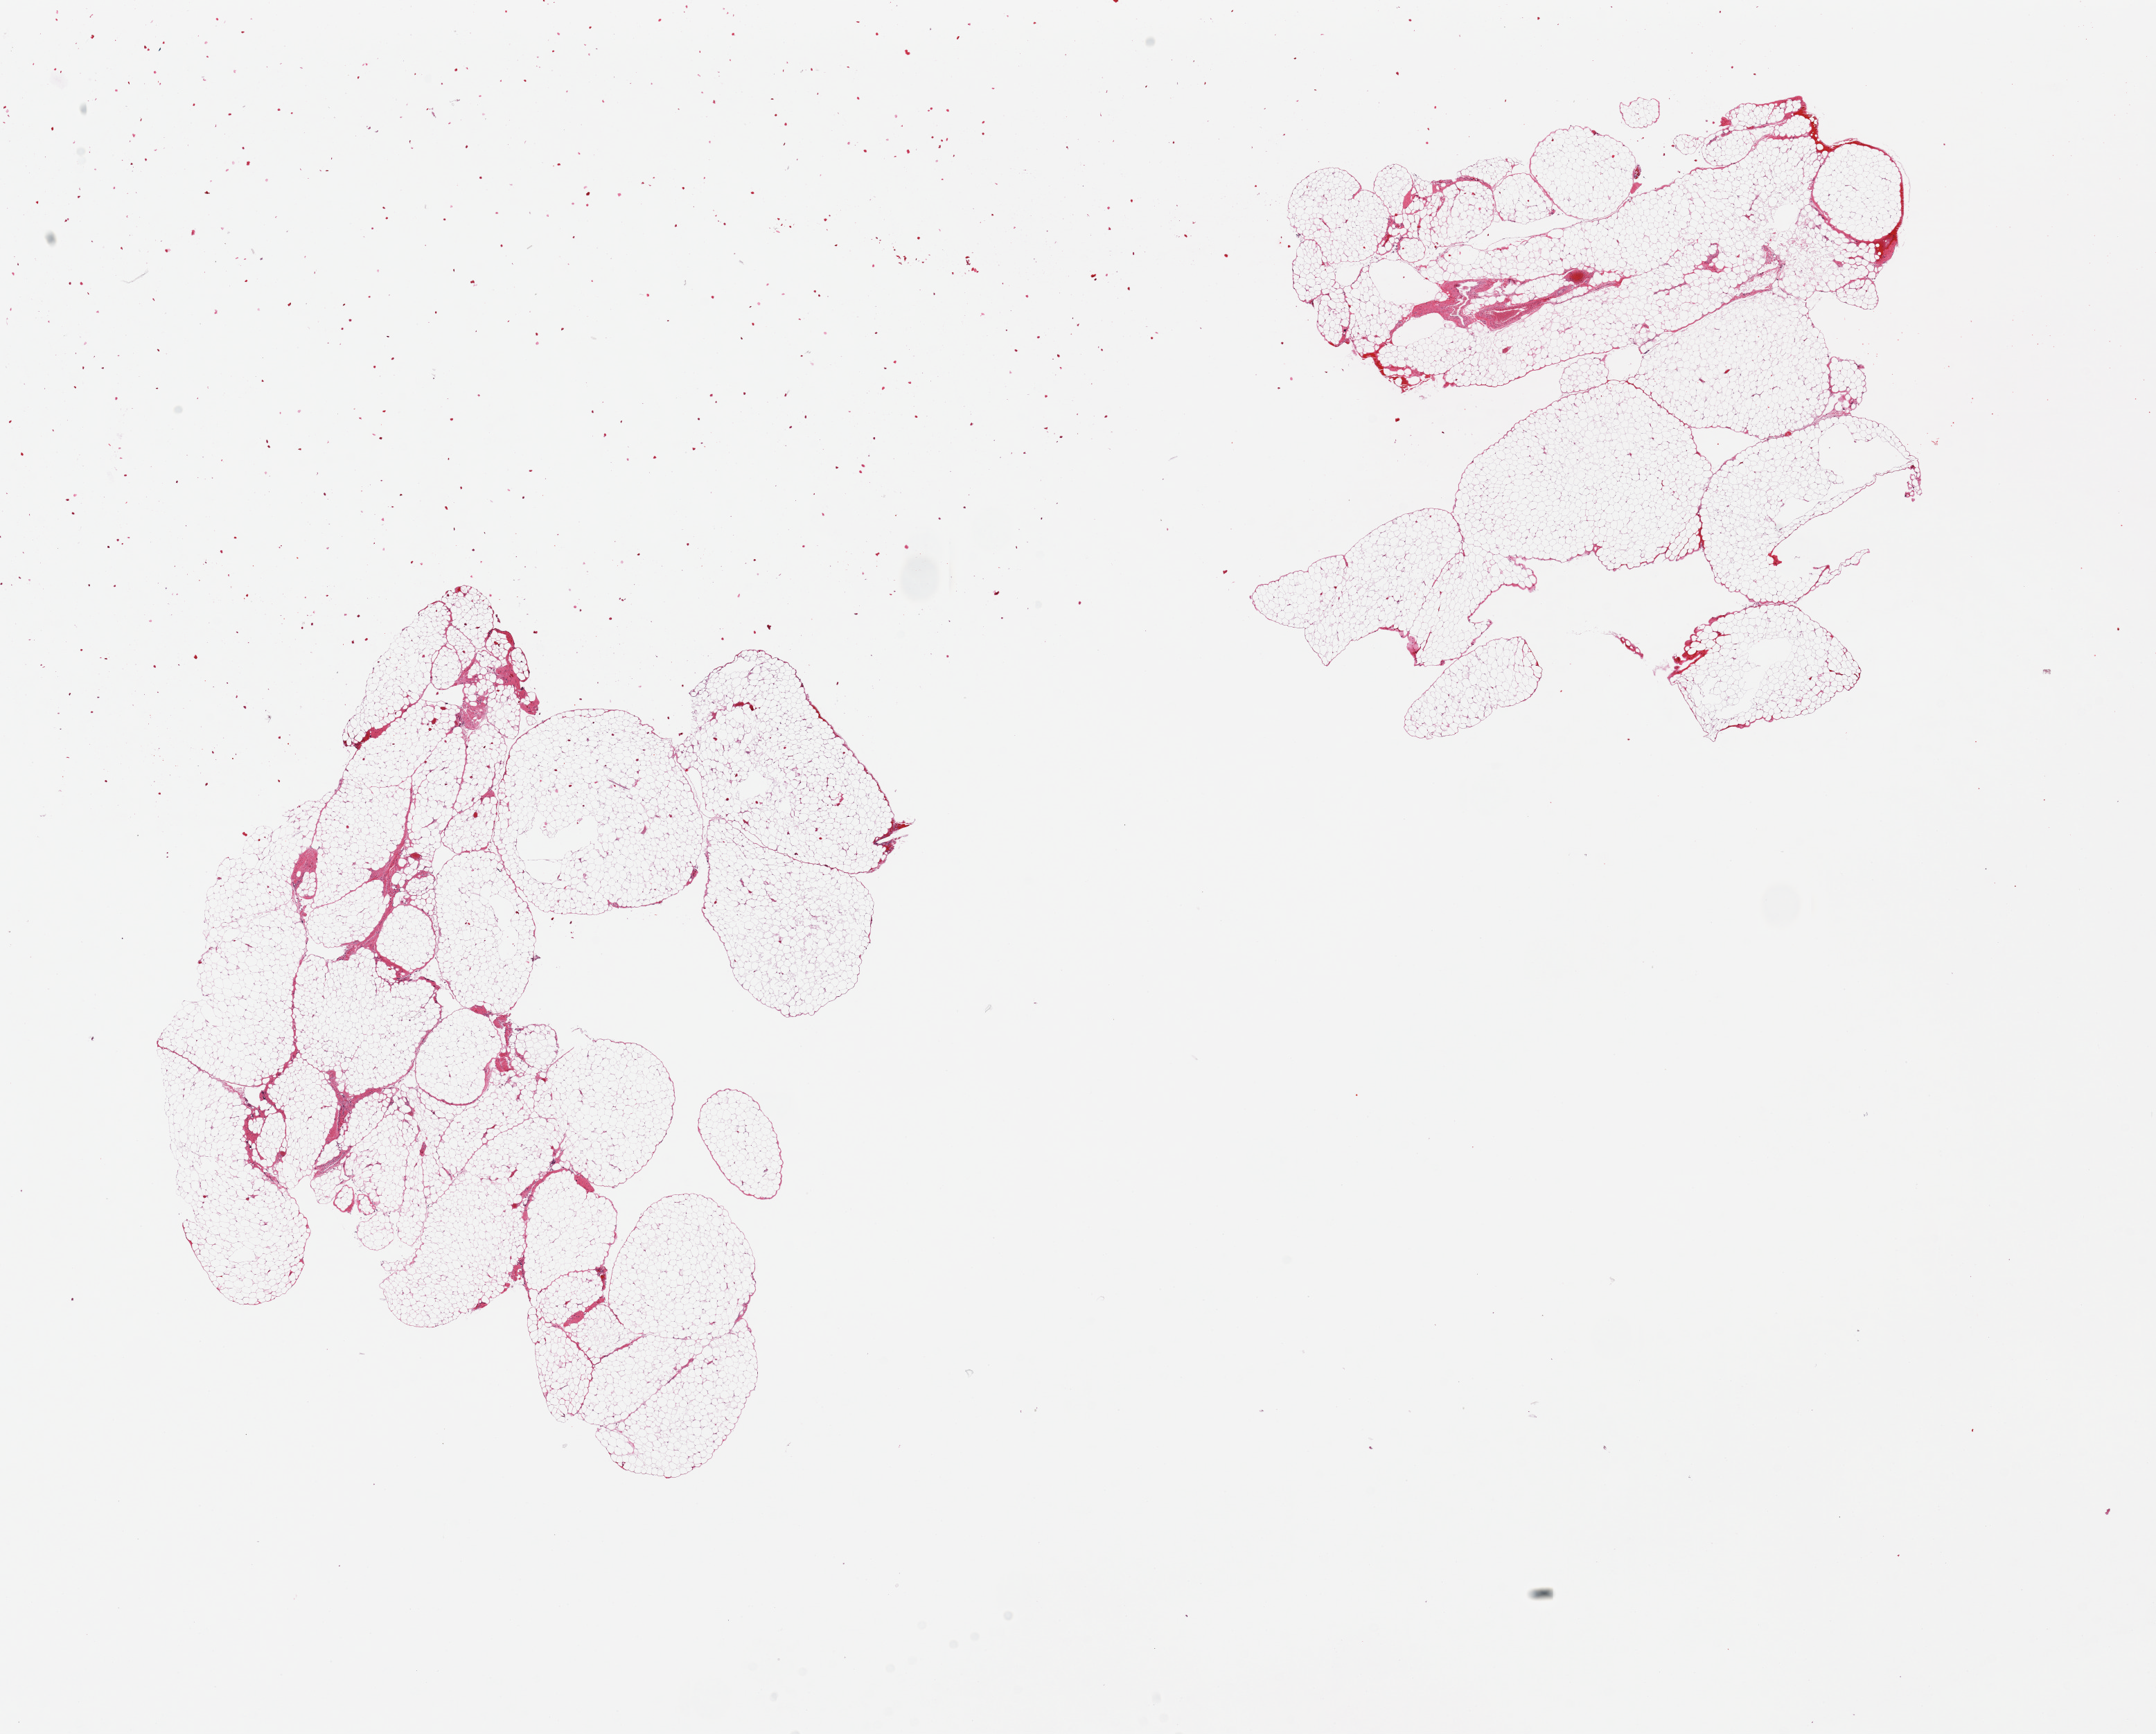
Digitized haematoxylin and eosin-stained section, whole scanned area (about 24.6 x 19.8 mm) shown as a low-resolution overview. PAXgene-fixed paraffin-embedded (PFPE) section. Section of omentum (target tissue). Tissue donor sample. Donor sex: male.
- pathologist's review note for this sample: 2 pieces